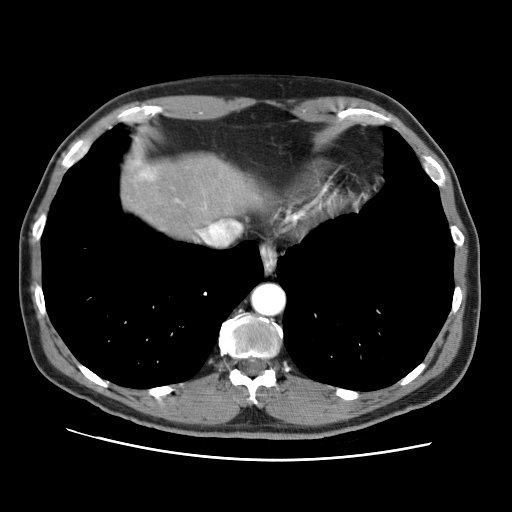
Contrast-enhanced abdominal CT (liver protocol), one axial slice; slice 64 of 71 in the series (ordered by position); reconstruction kernel STANDARD; soft-tissue window (W 400 / L 40 HU); 2.5 mm slice thickness; 512 × 512 image matrix. Case-level facts recorded for this patient, not image findings: diagnosis: hepatocellular carcinoma (patient treated with transarterial chemoembolisation; whether this scan precedes or follows treatment is not stated here); TNM stage (as recorded): Stage-II; Child-Pugh class: A; tumour differentiation: well differentiated; tumour size: 4.6 cm.
Annotated regions visible in this slice (semi-automatic segmentation, software-assisted and operator-edited):
- liver parenchyma outside the tumour (the mass and vessels are separate outlines, so this box may not span the whole liver): bounding box <122,156,262,230> (left, top, right, bottom; pixels)
- liver vessels: <137,163,153,179>